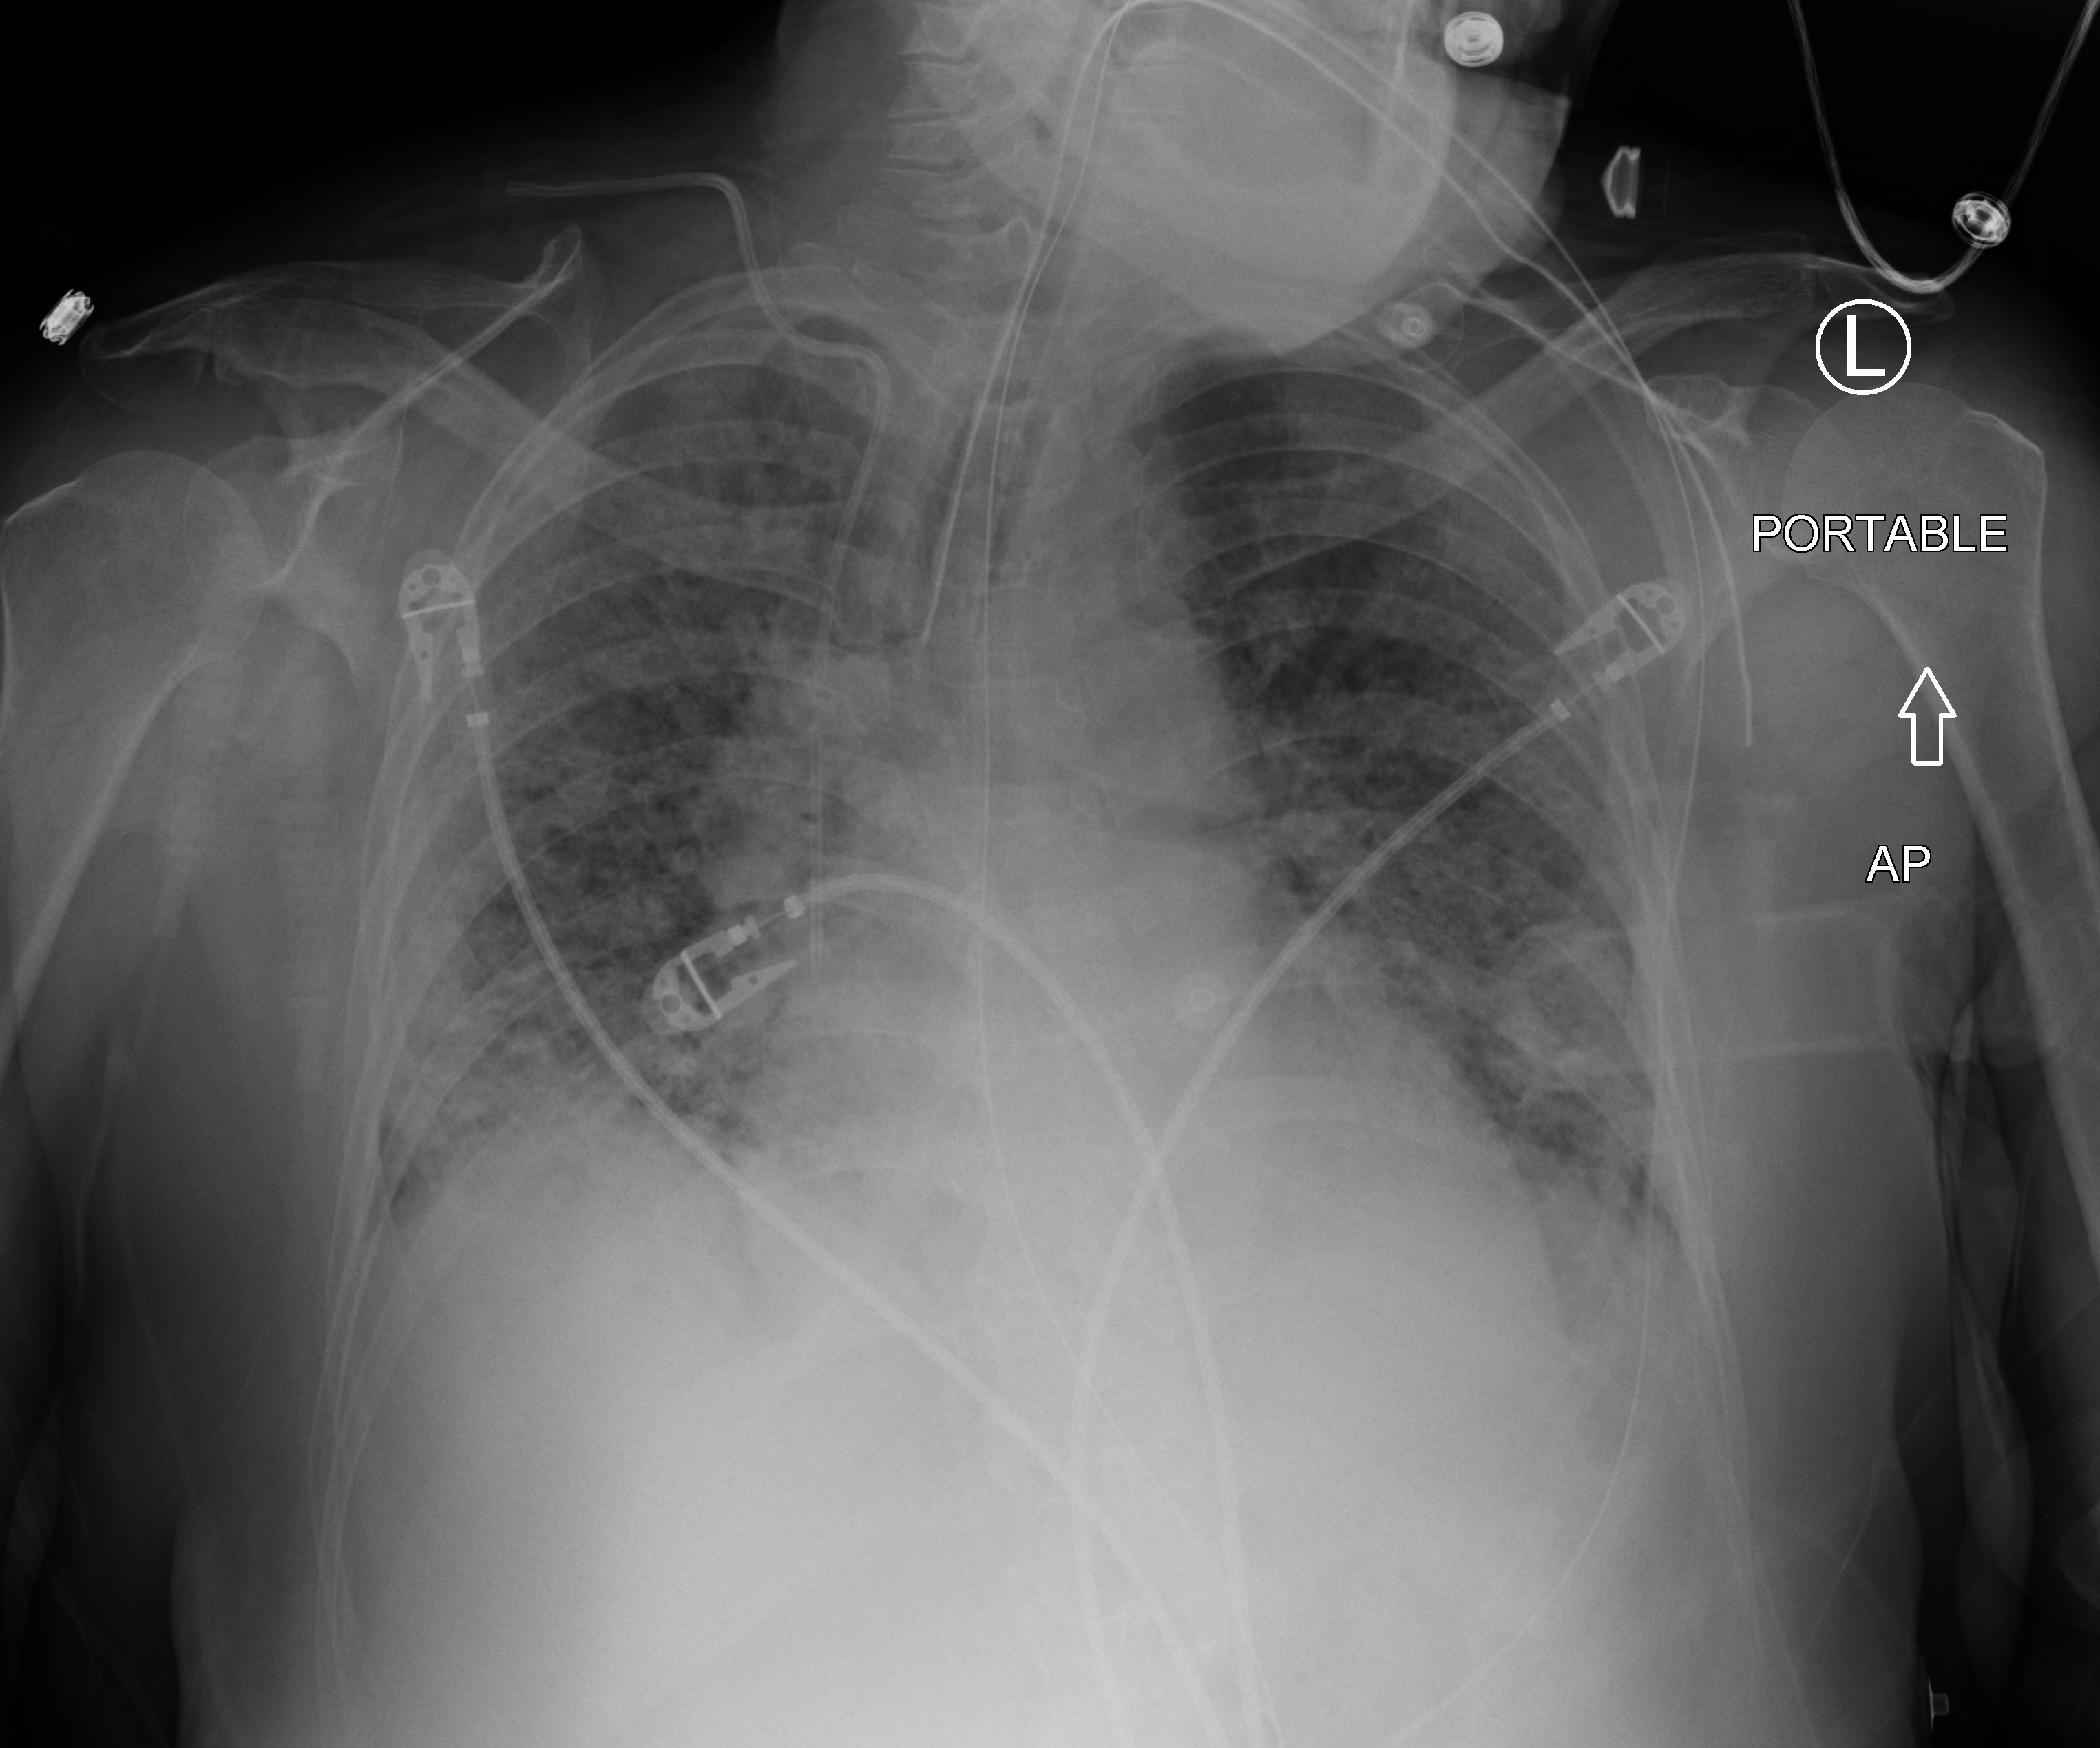
Portable chest radiograph; anteroposterior (AP) projection. Female patient hospitalised with COVID-19, age 60–74 years.
From the hospital-stay record, not from the radiograph (when in the stay this image was taken is not recorded):
- diabetes (admission record): no